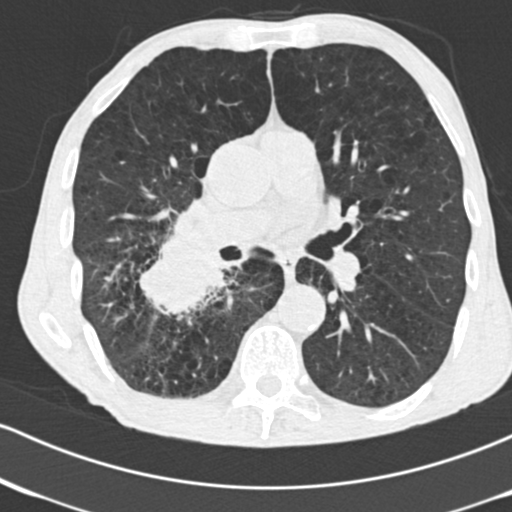
Axial slice from a low-dose chest CT screening exam. Second screening round (one year after baseline). Lung window (W 1500 / L -600 HU). 2 mm slice thickness. Standard (soft-tissue) reconstruction kernel (B30f). 120 kVp. 512 × 512 image matrix. Male participant, aged 64 years at enrolment.
Expert reader's lesion annotation, box from (x=131, y=230) to (x=239, y=330) px. Reader record for this screening exam (exam-level; its link to the box is not recorded): non-calcified nodule or mass ≥4 mm, 52 × 37 mm, spiculated (stellate) margins, soft tissue attenuation, pre-existing on the prior screen: no.